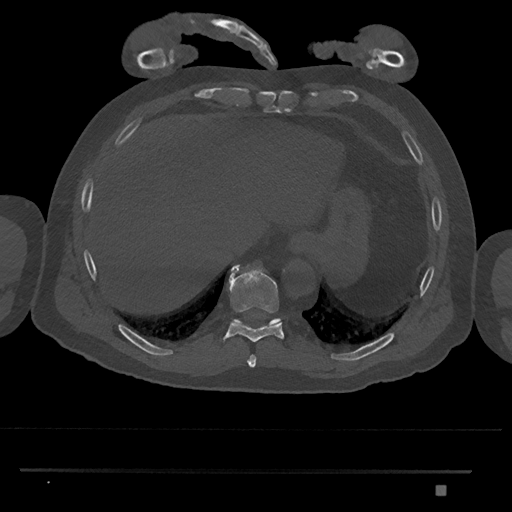
CT including the spine, one axial slice. Slice 1048 of 1134 in the series (ordered by position). Reconstruction kernel Br40s/3. 120 kVp. Bone window (W 1800 / L 400 HU). 0.5 mm slice thickness. 512 × 512 image matrix, field of view 429 × 429 mm. Patient: male, 65 years. From the clinical record (not read from this slice): primary cancer: prostate.
Outlined on this slice (semi-automatically segmented with operator editing):
- T10 vertebra: bounding box <232,318,281,324> (left, top, right, bottom; pixels)
- T8 vertebra: <247,355,256,367>
- T9 vertebra: <225,264,284,343>